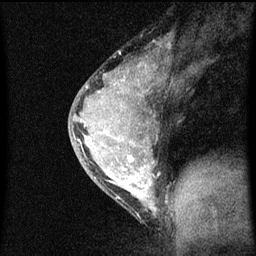
Breast MRI (dynamic contrast-enhanced), one sagittal slice. Dynamic contrast-enhanced series, image 2 of 3 at this slice position (ordered by acquisition). 1.5 T. TE 4.2 ms, TR 8 ms. 2 mm slice thickness. 256 × 256 image matrix, field of view 180 × 180 mm. Female patient, age 33 years.
Annotated regions visible in this slice (semi-automatically segmented with operator editing):
- analysis volume of interest (the breast-tissue region the enhancement analysis was run in; not a lesion): box from (x=69, y=56) to (x=170, y=215) px
- tumour enhancement mask (voxels above the 70 % enhancement threshold inside the analysis volume of interest): (x=79, y=64)–(x=157, y=209)